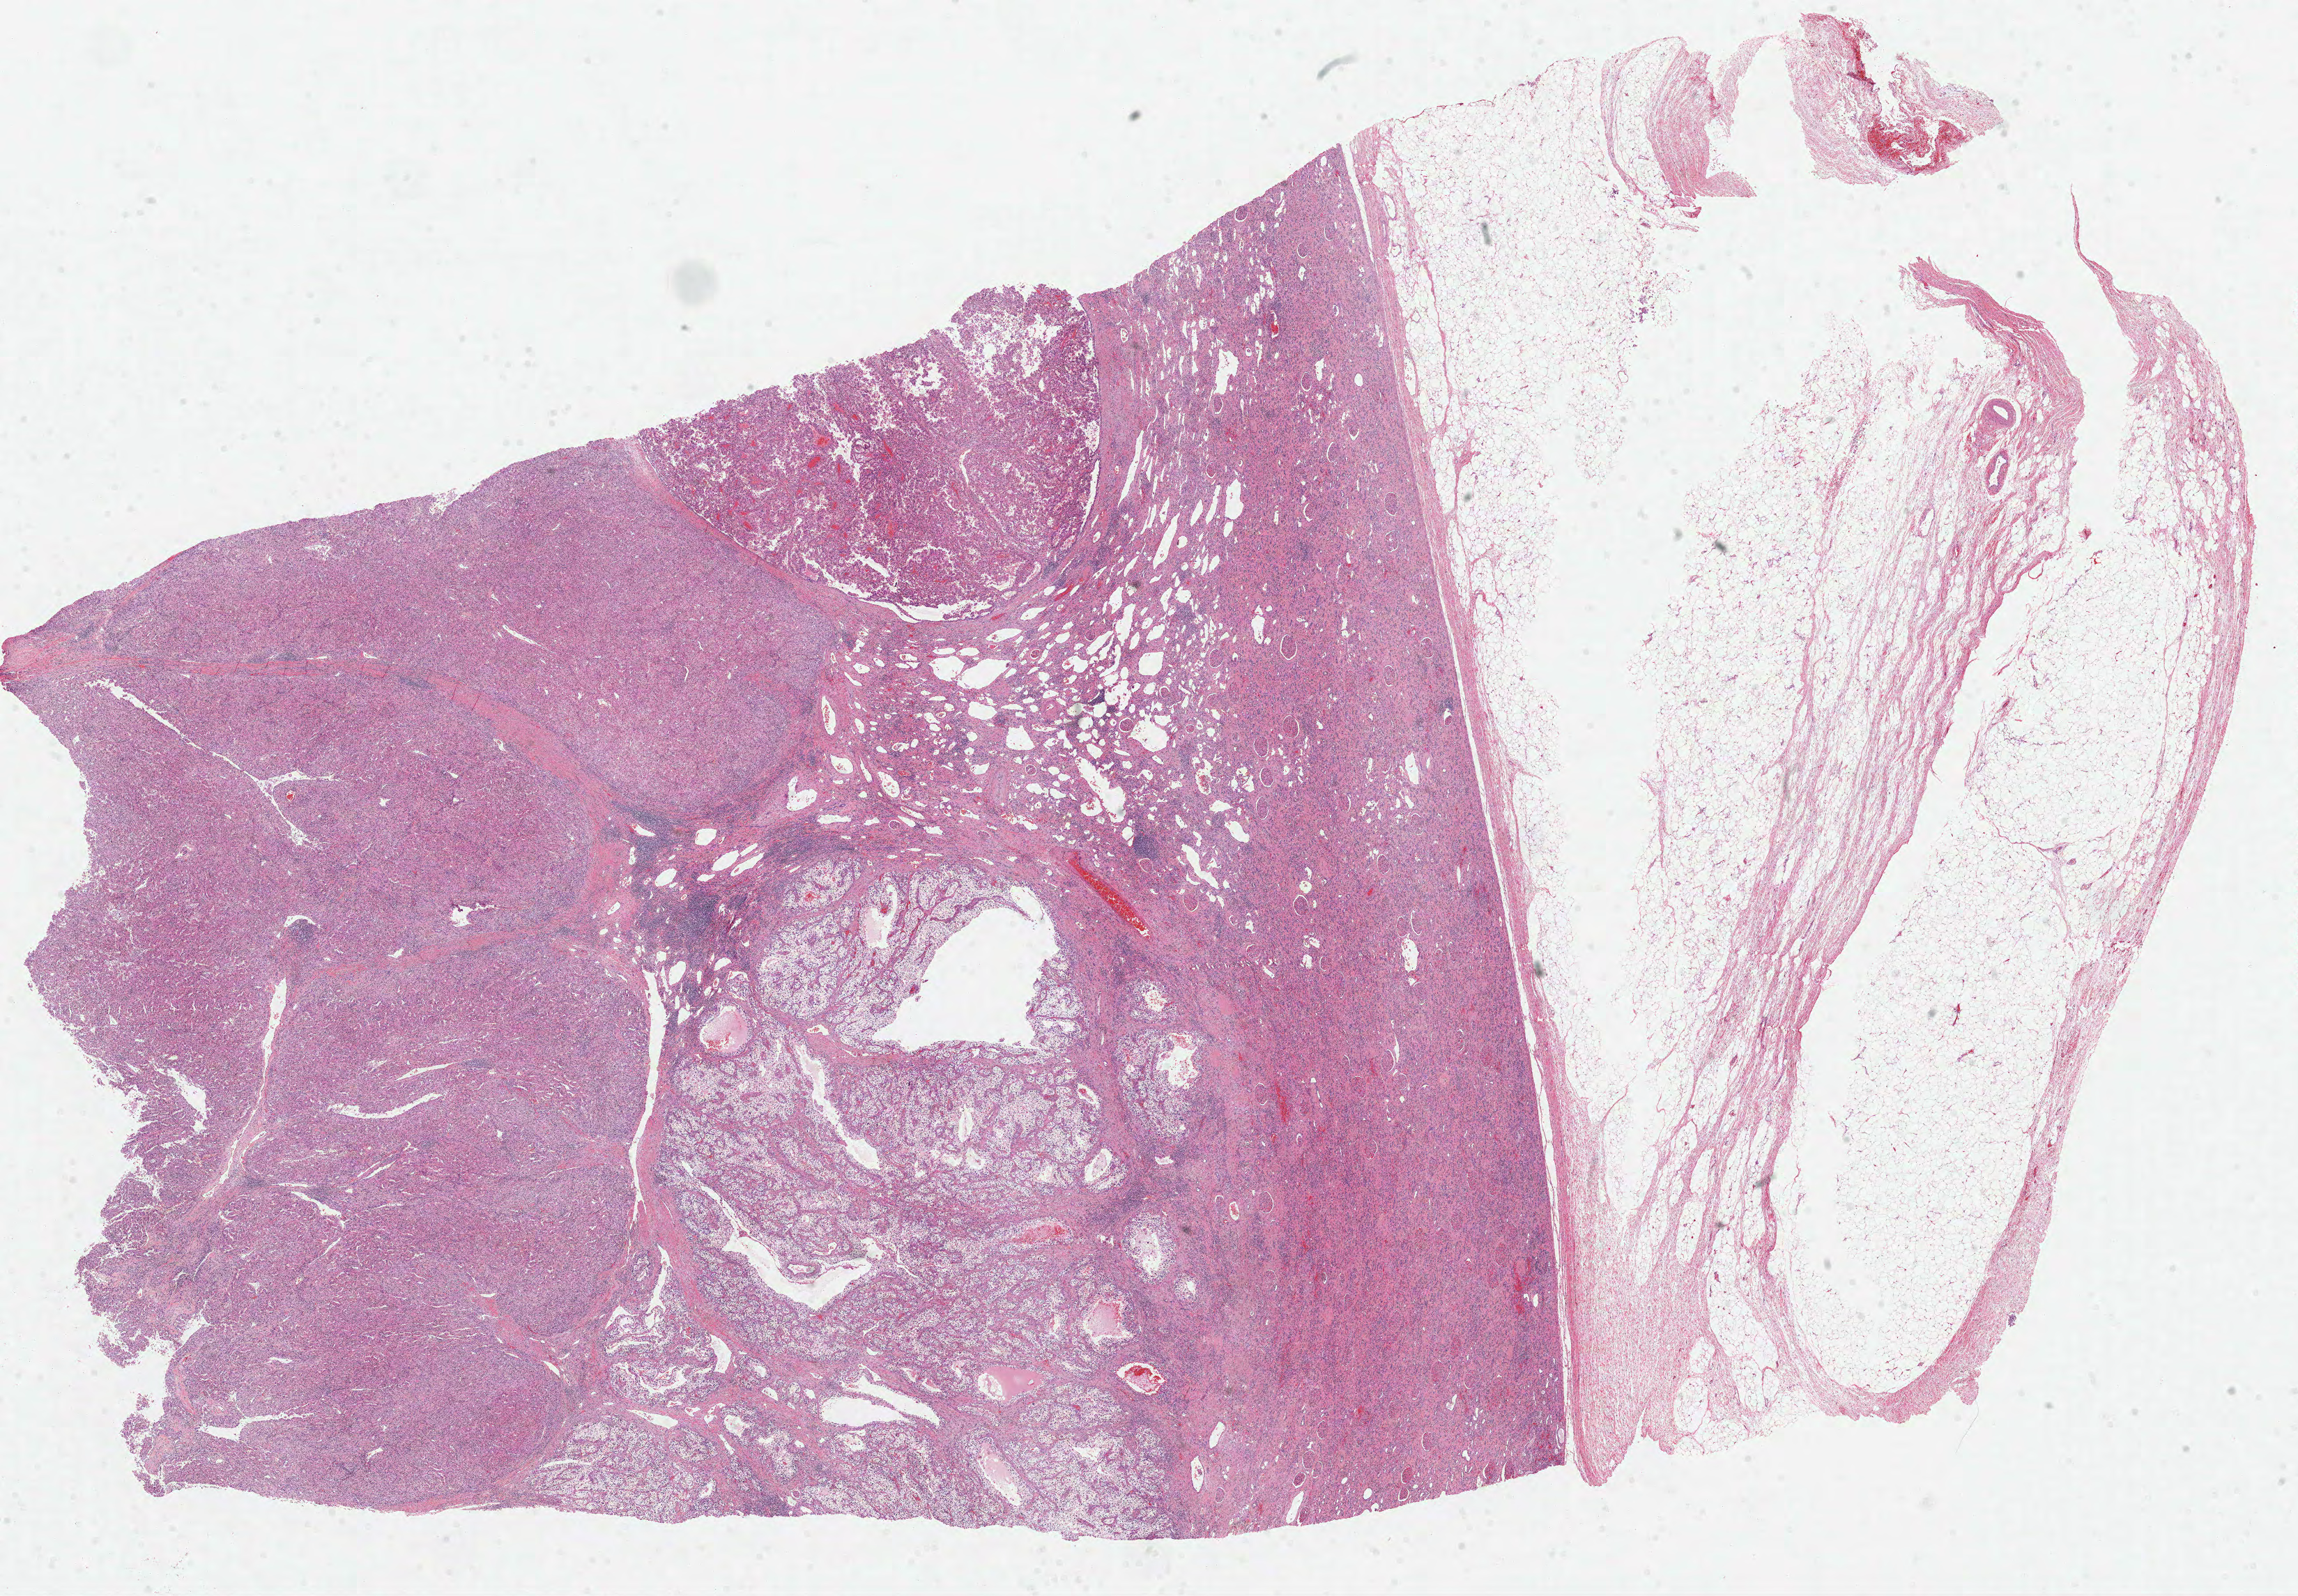
Whole-slide histology image, H&E — a low-resolution overview of the entire scanned area, about 26.6 x 18.5 mm (acquisition: 40x scan), formalin-fixed paraffin-embedded (FFPE) diagnostic section, primary tumour sample from the kidney. Male patient; age at initial diagnosis 55 years. Histologic grade: G3 (poorly differentiated).
Histologic diagnosis: Clear cell adenocarcinoma, NOS. TNM: T2 N0 M1. AJCC pathologic stage: IV.